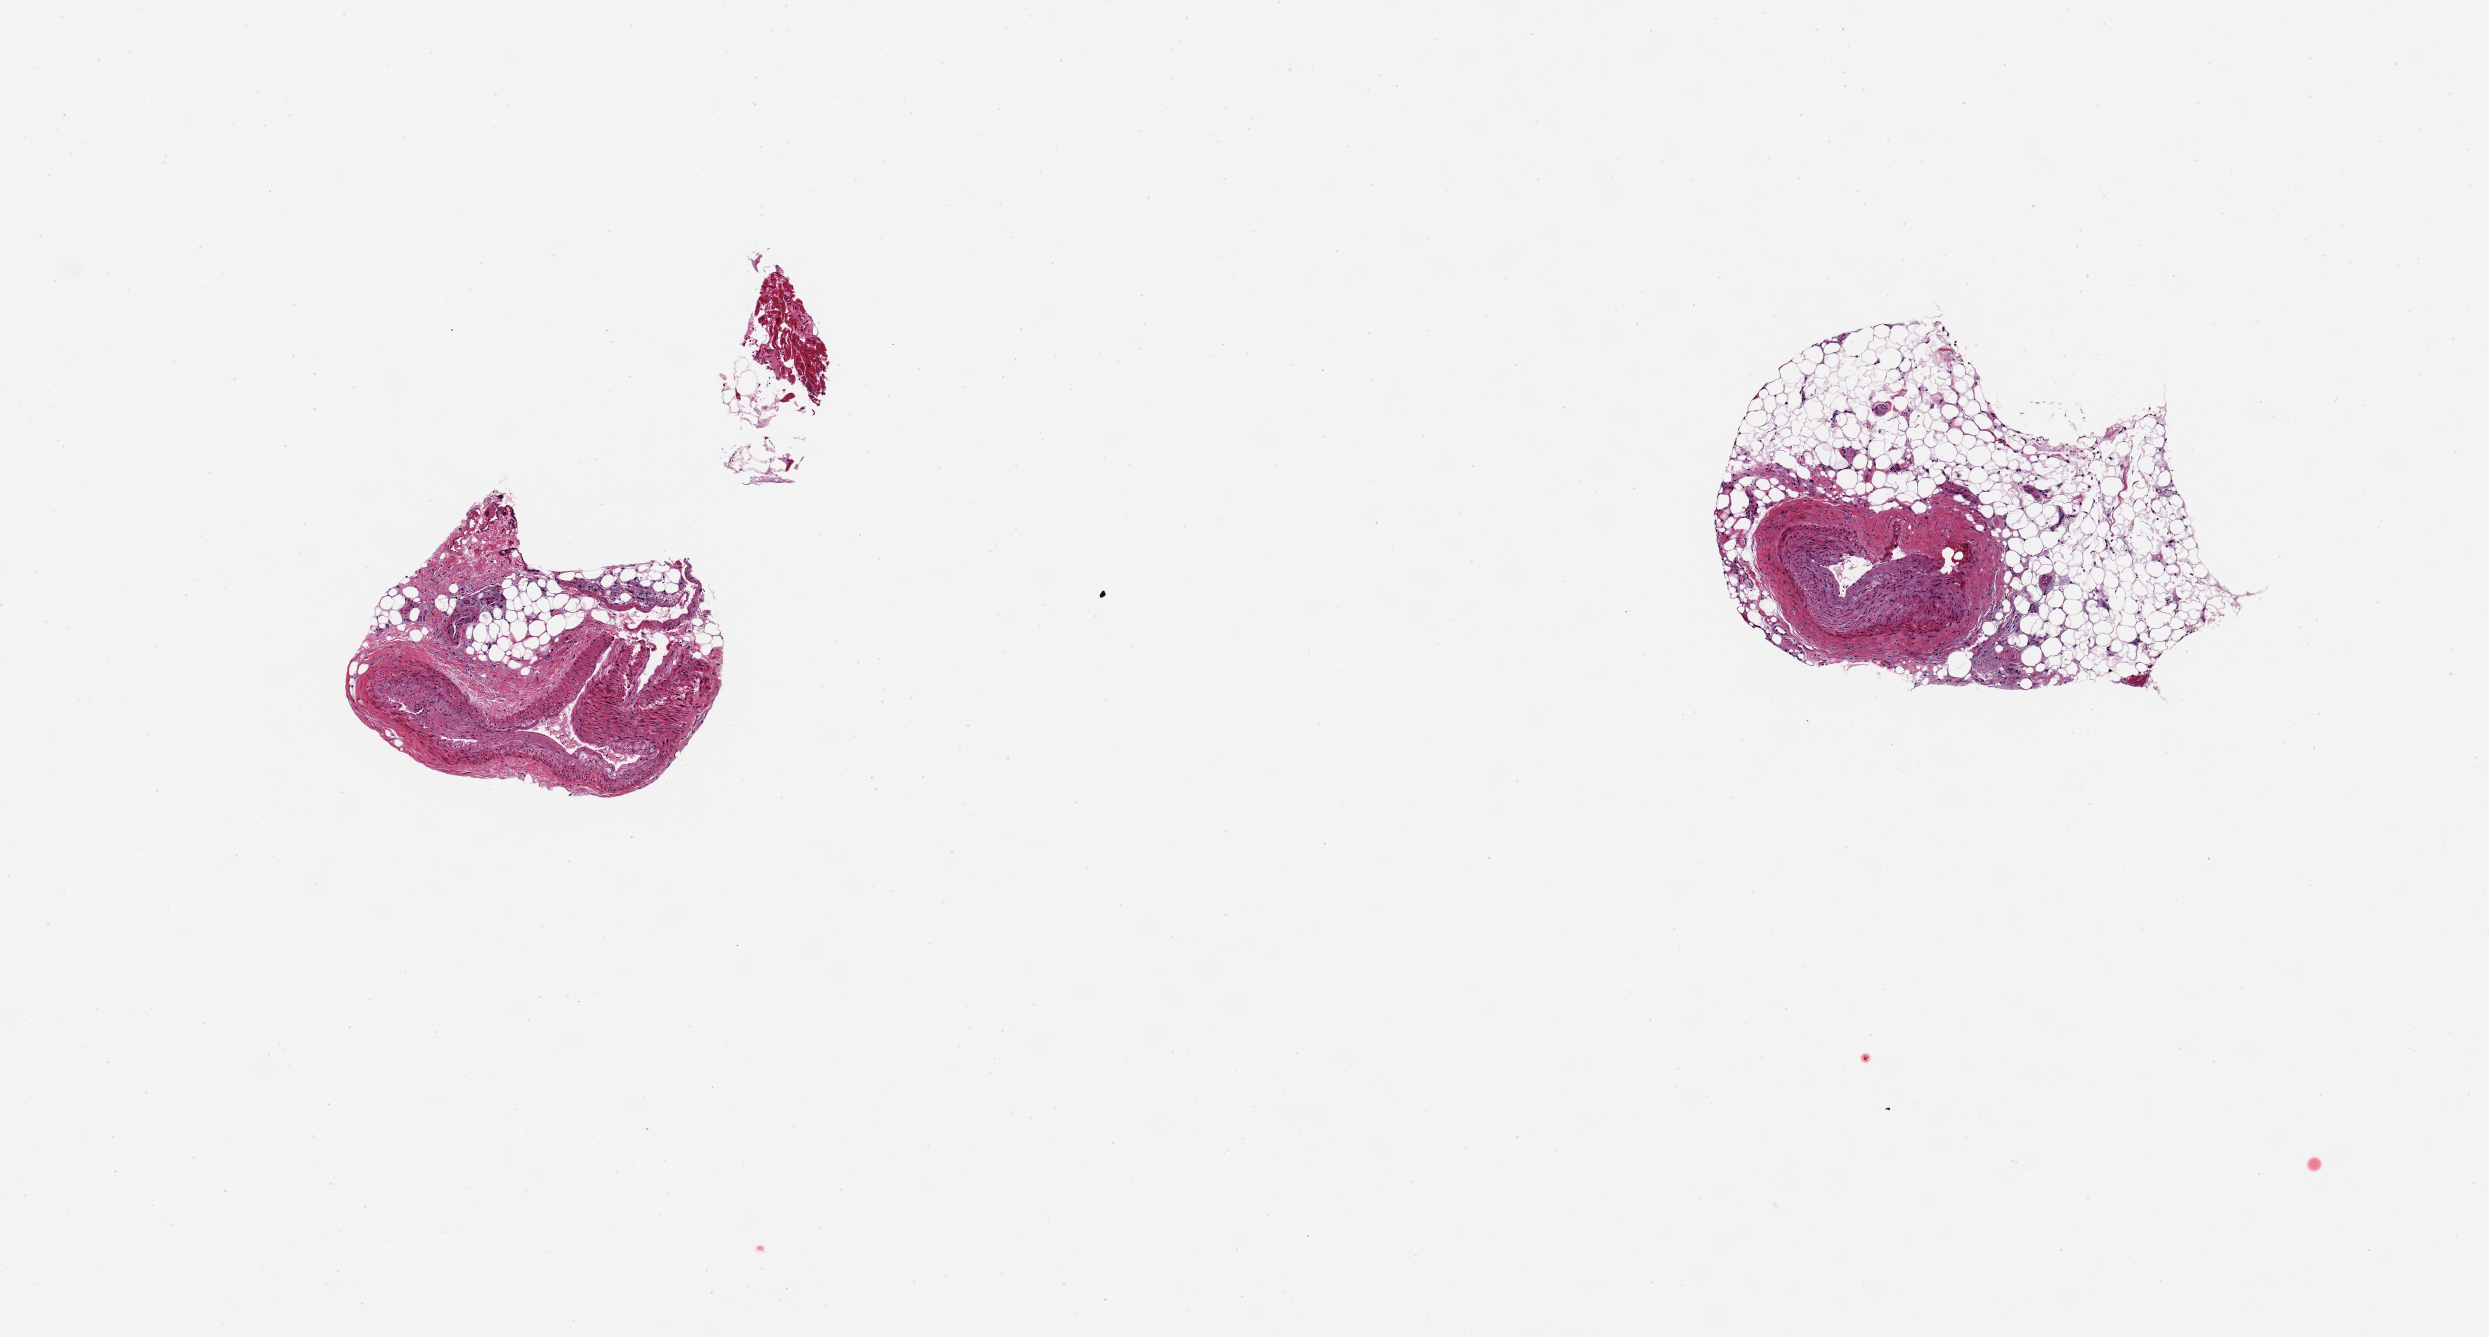
Haematoxylin and eosin whole-slide image, brightfield — shown as a low-resolution overview of the whole scanned area (about 9.8 x 5.3 mm, acquisition: 20x scan). PAXgene-fixed paraffin-embedded (PFPE) section. Target tissue: coronary artery. Donor tissue sample. Donor: male.
Review note (as recorded): 2 pieces, 1x1.2 & 1.8x1.4mm; 1 mm arteries with moderate fibrous plaques; 30-60% external adipose.